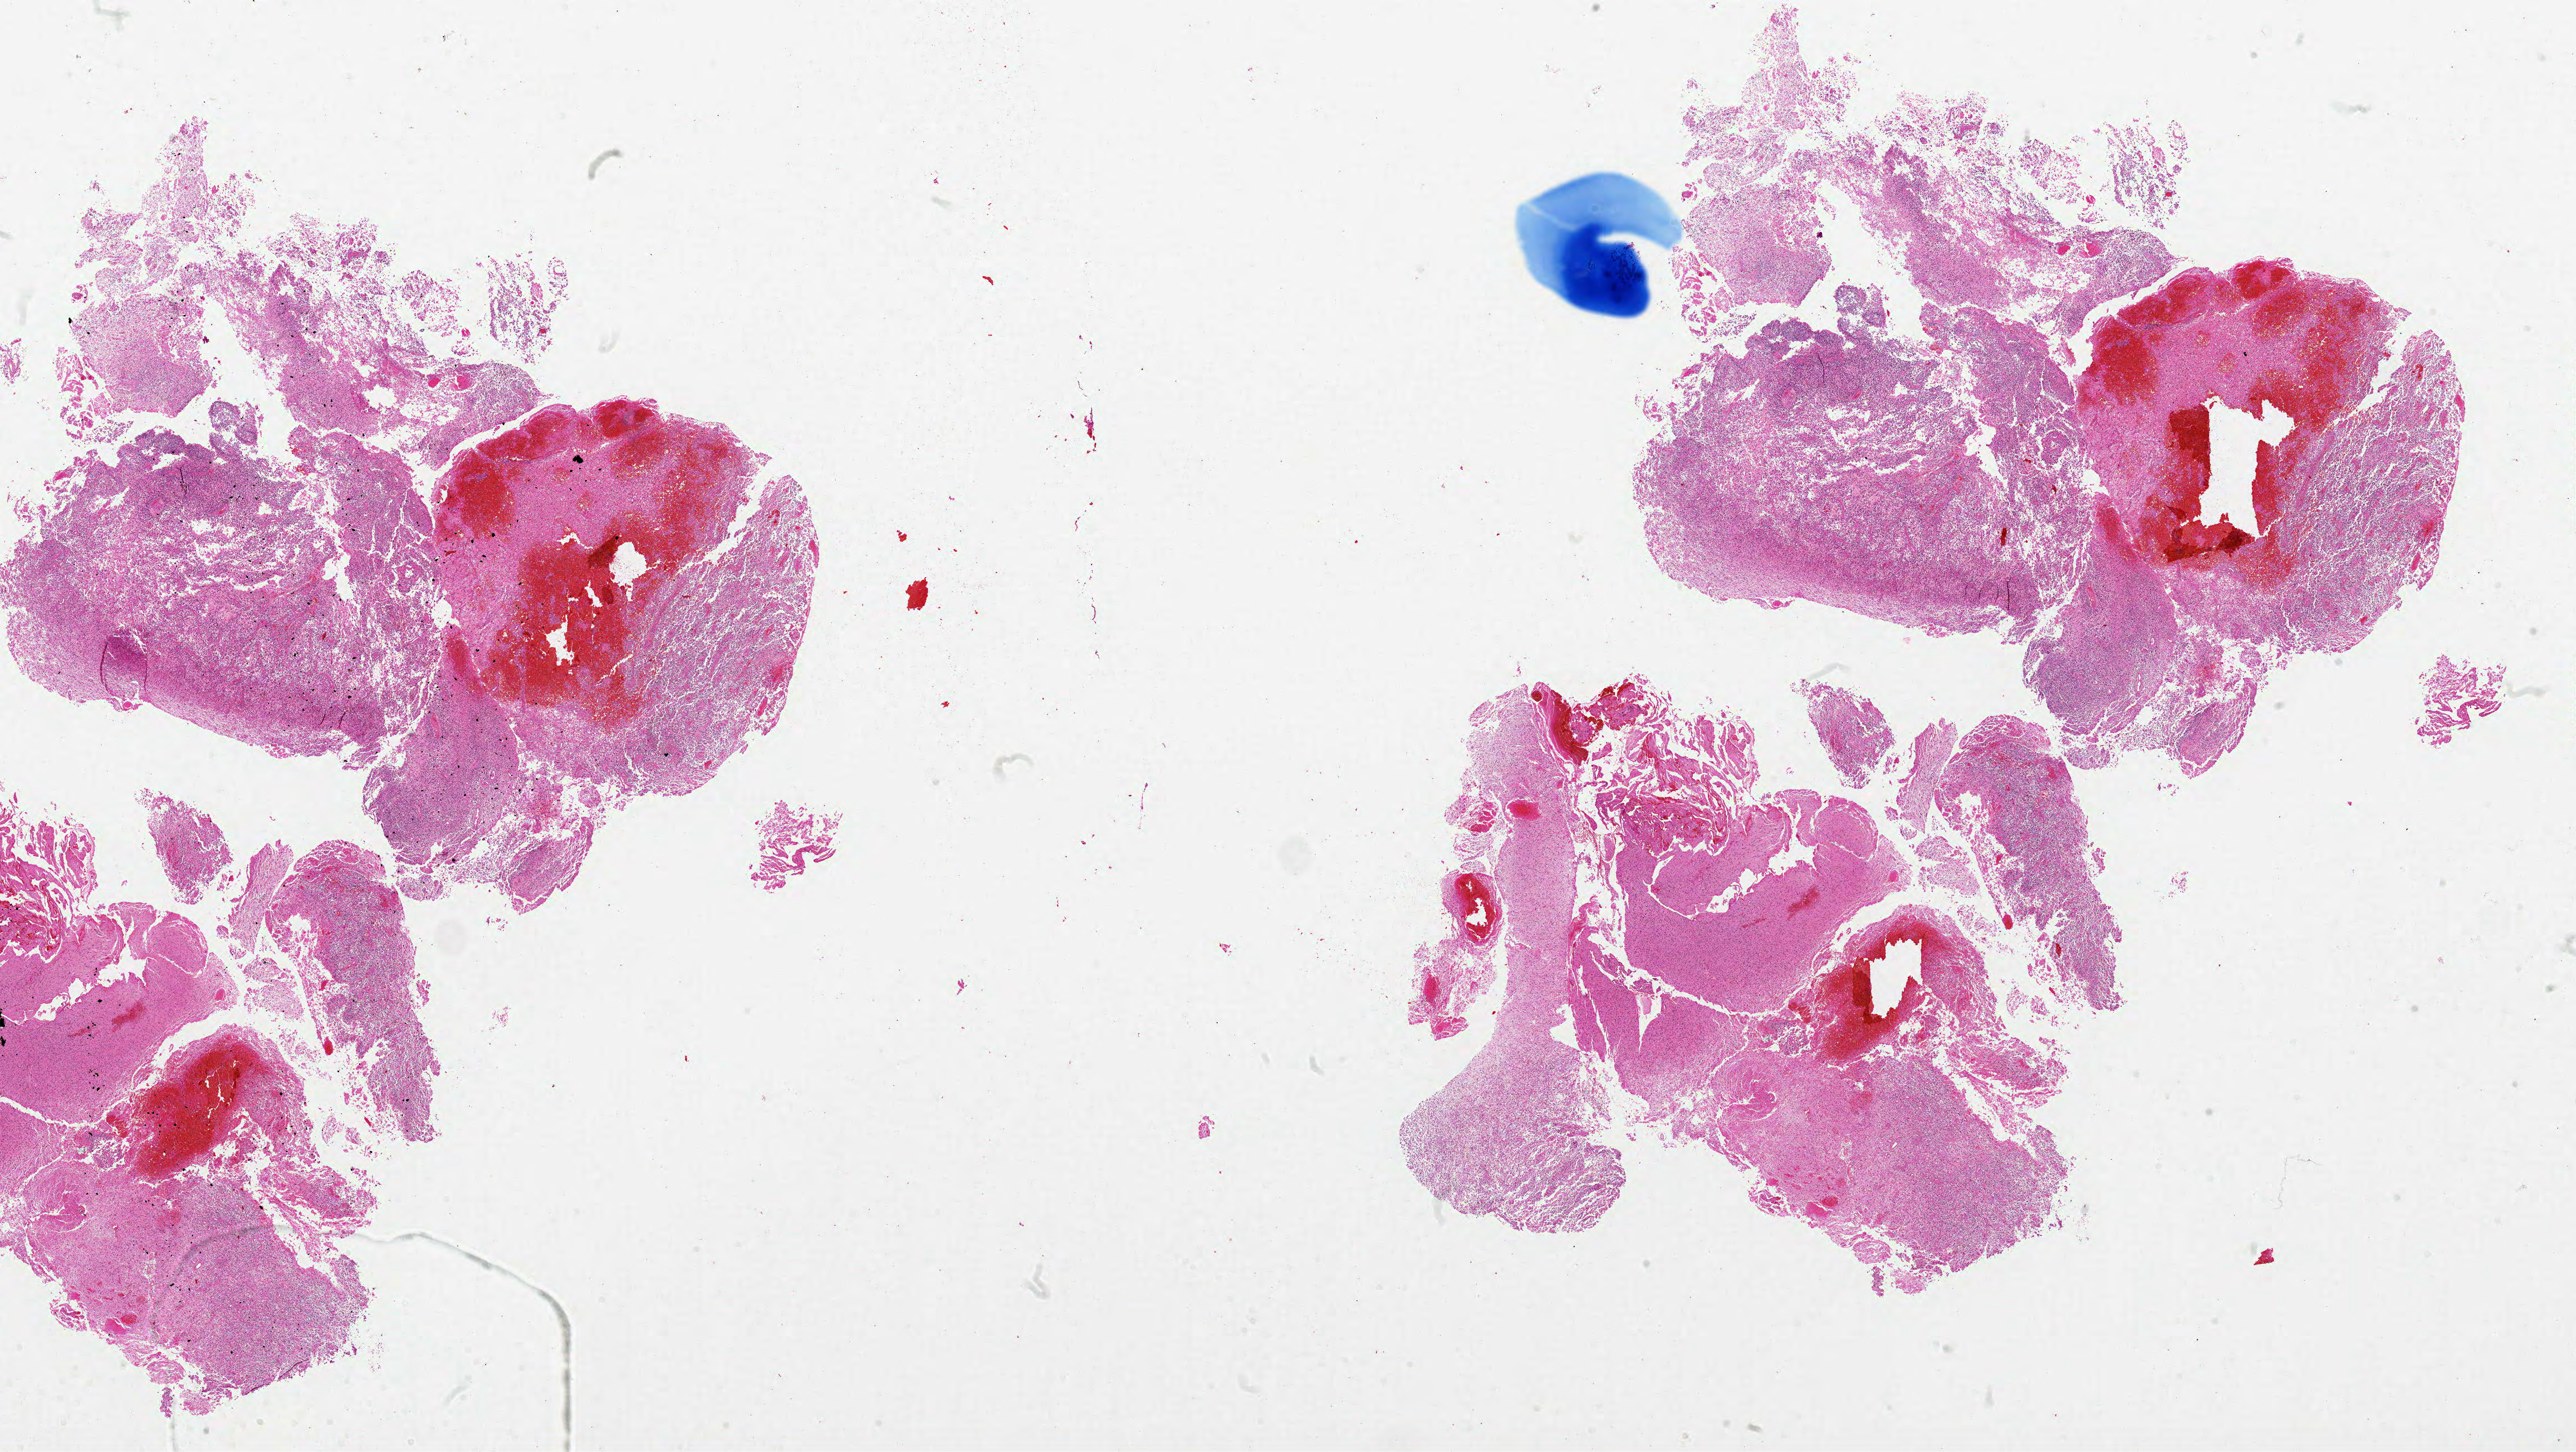
Digitized H&E tissue section (whole slide) — shown as a low-resolution overview of the whole scanned area (about 37.0 x 20.8 mm, from a 20x scan); FFPE section; primary tumour sample from the brain. Female patient; age at initial diagnosis 36 years.
Pathologic diagnosis: Glioblastoma.